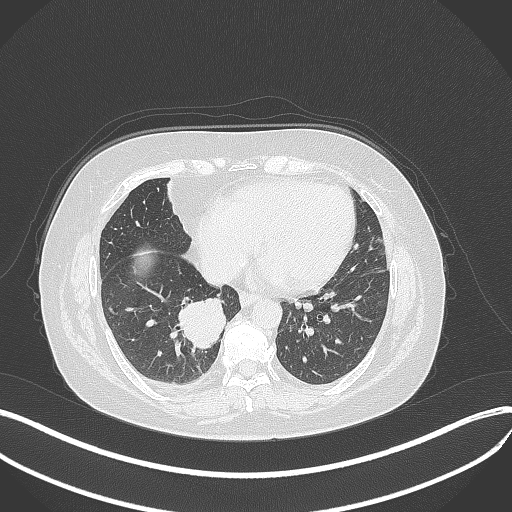
Chest CT, one axial slice. Slice 127 of 381 in the series (ordered by position). 120 kVp. Lung window (W 1500 / L -600 HU). 1 mm slice thickness. 512 × 512 image matrix. Patient: female, 56 years. From the clinical record (not read from this slice): clinical TNM (as recorded): T2b N1 M0; histopathological grade: G3.
Outlined on this slice (rectangle marked by the reading radiologist):
- lung tumour (recorded histology: small cell carcinoma): bounding box [x1, y1, x2, y2] px = [173, 293, 233, 351]